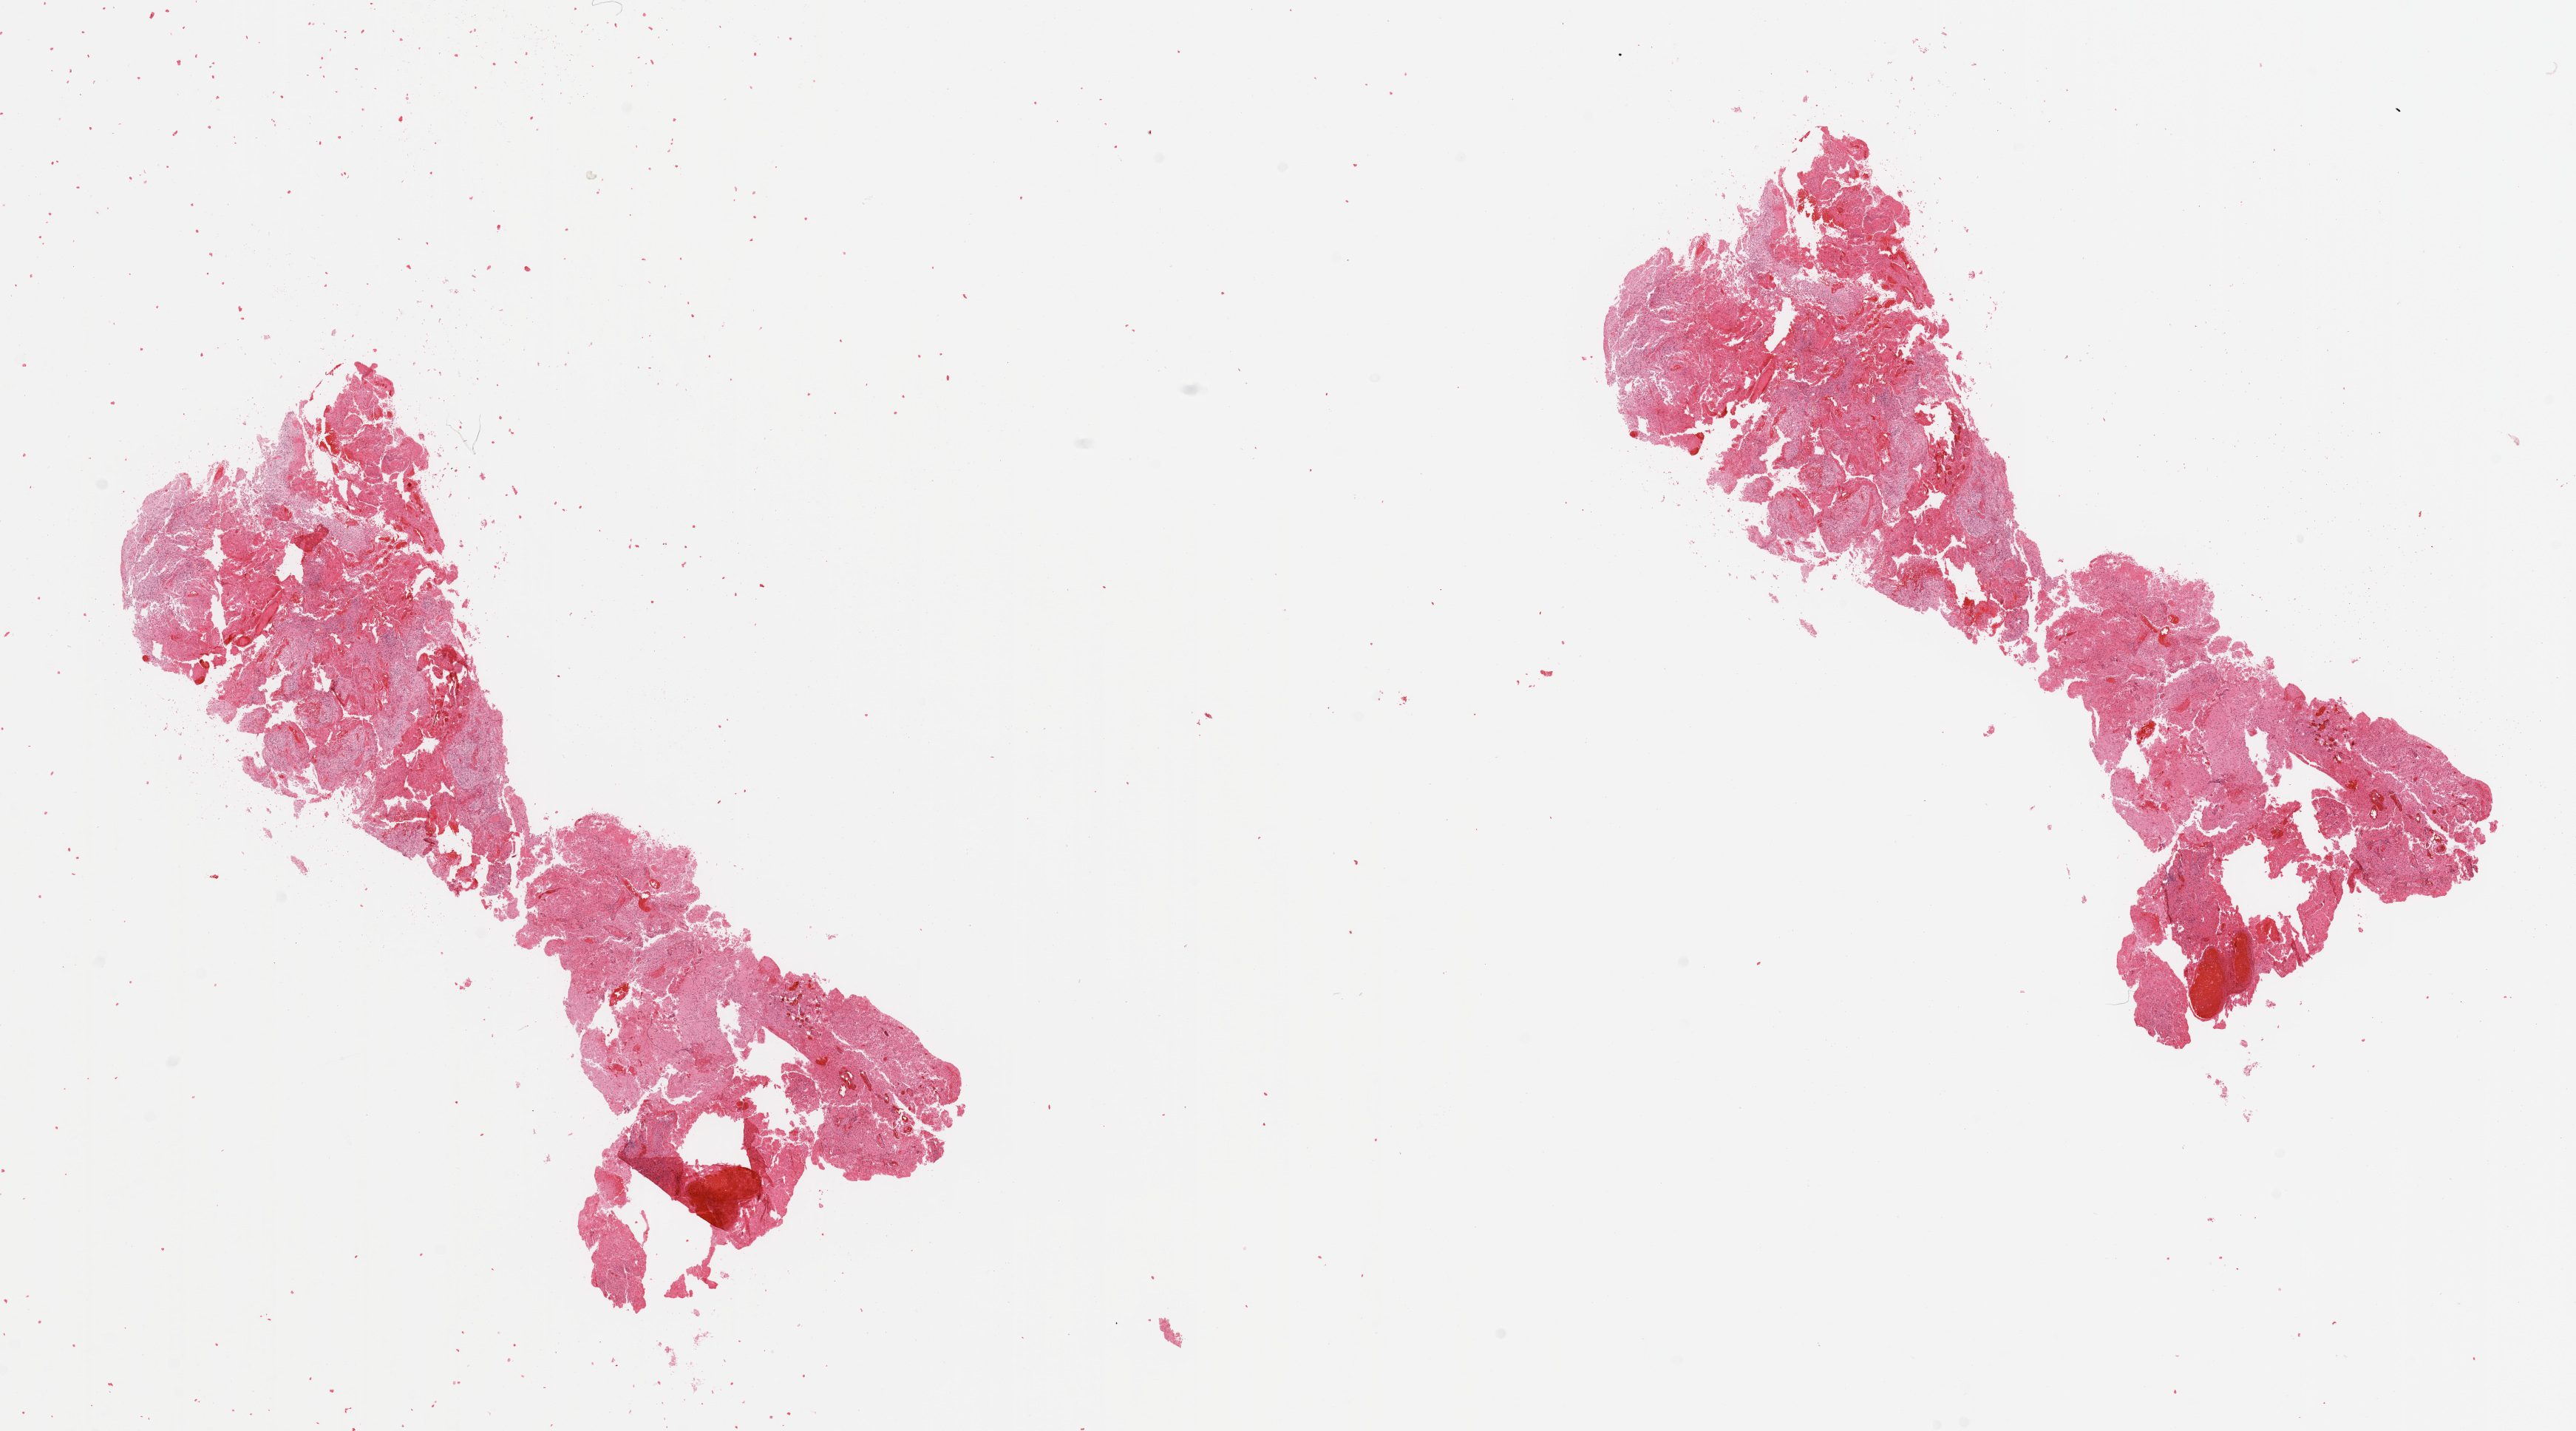
H&E-stained whole-slide image — a low-resolution overview of the entire scanned area, about 27.6 x 15.3 mm (acquisition: 20x scan), tumour tissue sample, sampled site: brain. Patient: male, age 74 years. Composition of this section per pathologist review: tumour nuclei 75%, necrosis 10%.
Diagnosis: Glioblastoma.